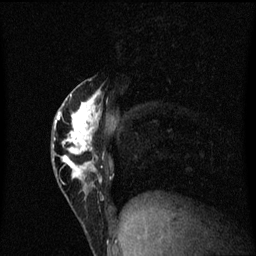
Breast MRI (dynamic contrast-enhanced), one sagittal slice. Position 25 of 60 along the scan axis. Dynamic contrast-enhanced series, image 2 of 3 at this slice position (ordered by acquisition). 1.5 T. TE 4.2 ms, TR 8.4 ms. 2 mm slice thickness. 256 × 256 image matrix, field of view 200 × 200 mm. Female patient, age 40 years.
Structures marked on this image (semi-automatically segmented with operator editing):
- analysis volume of interest (the breast-tissue region the enhancement analysis was run in; not a lesion): bounding box (x1, y1, x2, y2) in pixels: (52, 78, 106, 203)
- tumour enhancement mask (voxels above the 70 % enhancement threshold inside the analysis volume of interest): (55, 92, 102, 189)